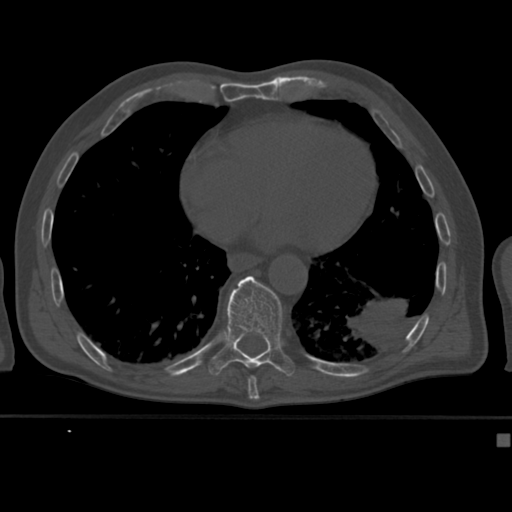
CT including the spine, one axial slice; reconstruction kernel Br40s; bone window (W 1800 / L 400 HU); 512 × 512 image matrix, field of view 337 × 337 mm. Patient: male, 64 years. From the clinical record (not read from this slice): primary cancer: uterus; vertebrae with lytic lesions (as recorded): T1, T4, T5, T7, L5.
Annotated regions visible in this slice (semi-automatically segmented with operator editing):
- T10 vertebra: bounding box [x1, y1, x2, y2] px = [208, 276, 295, 377]
- T9 vertebra: [248, 376, 257, 382]